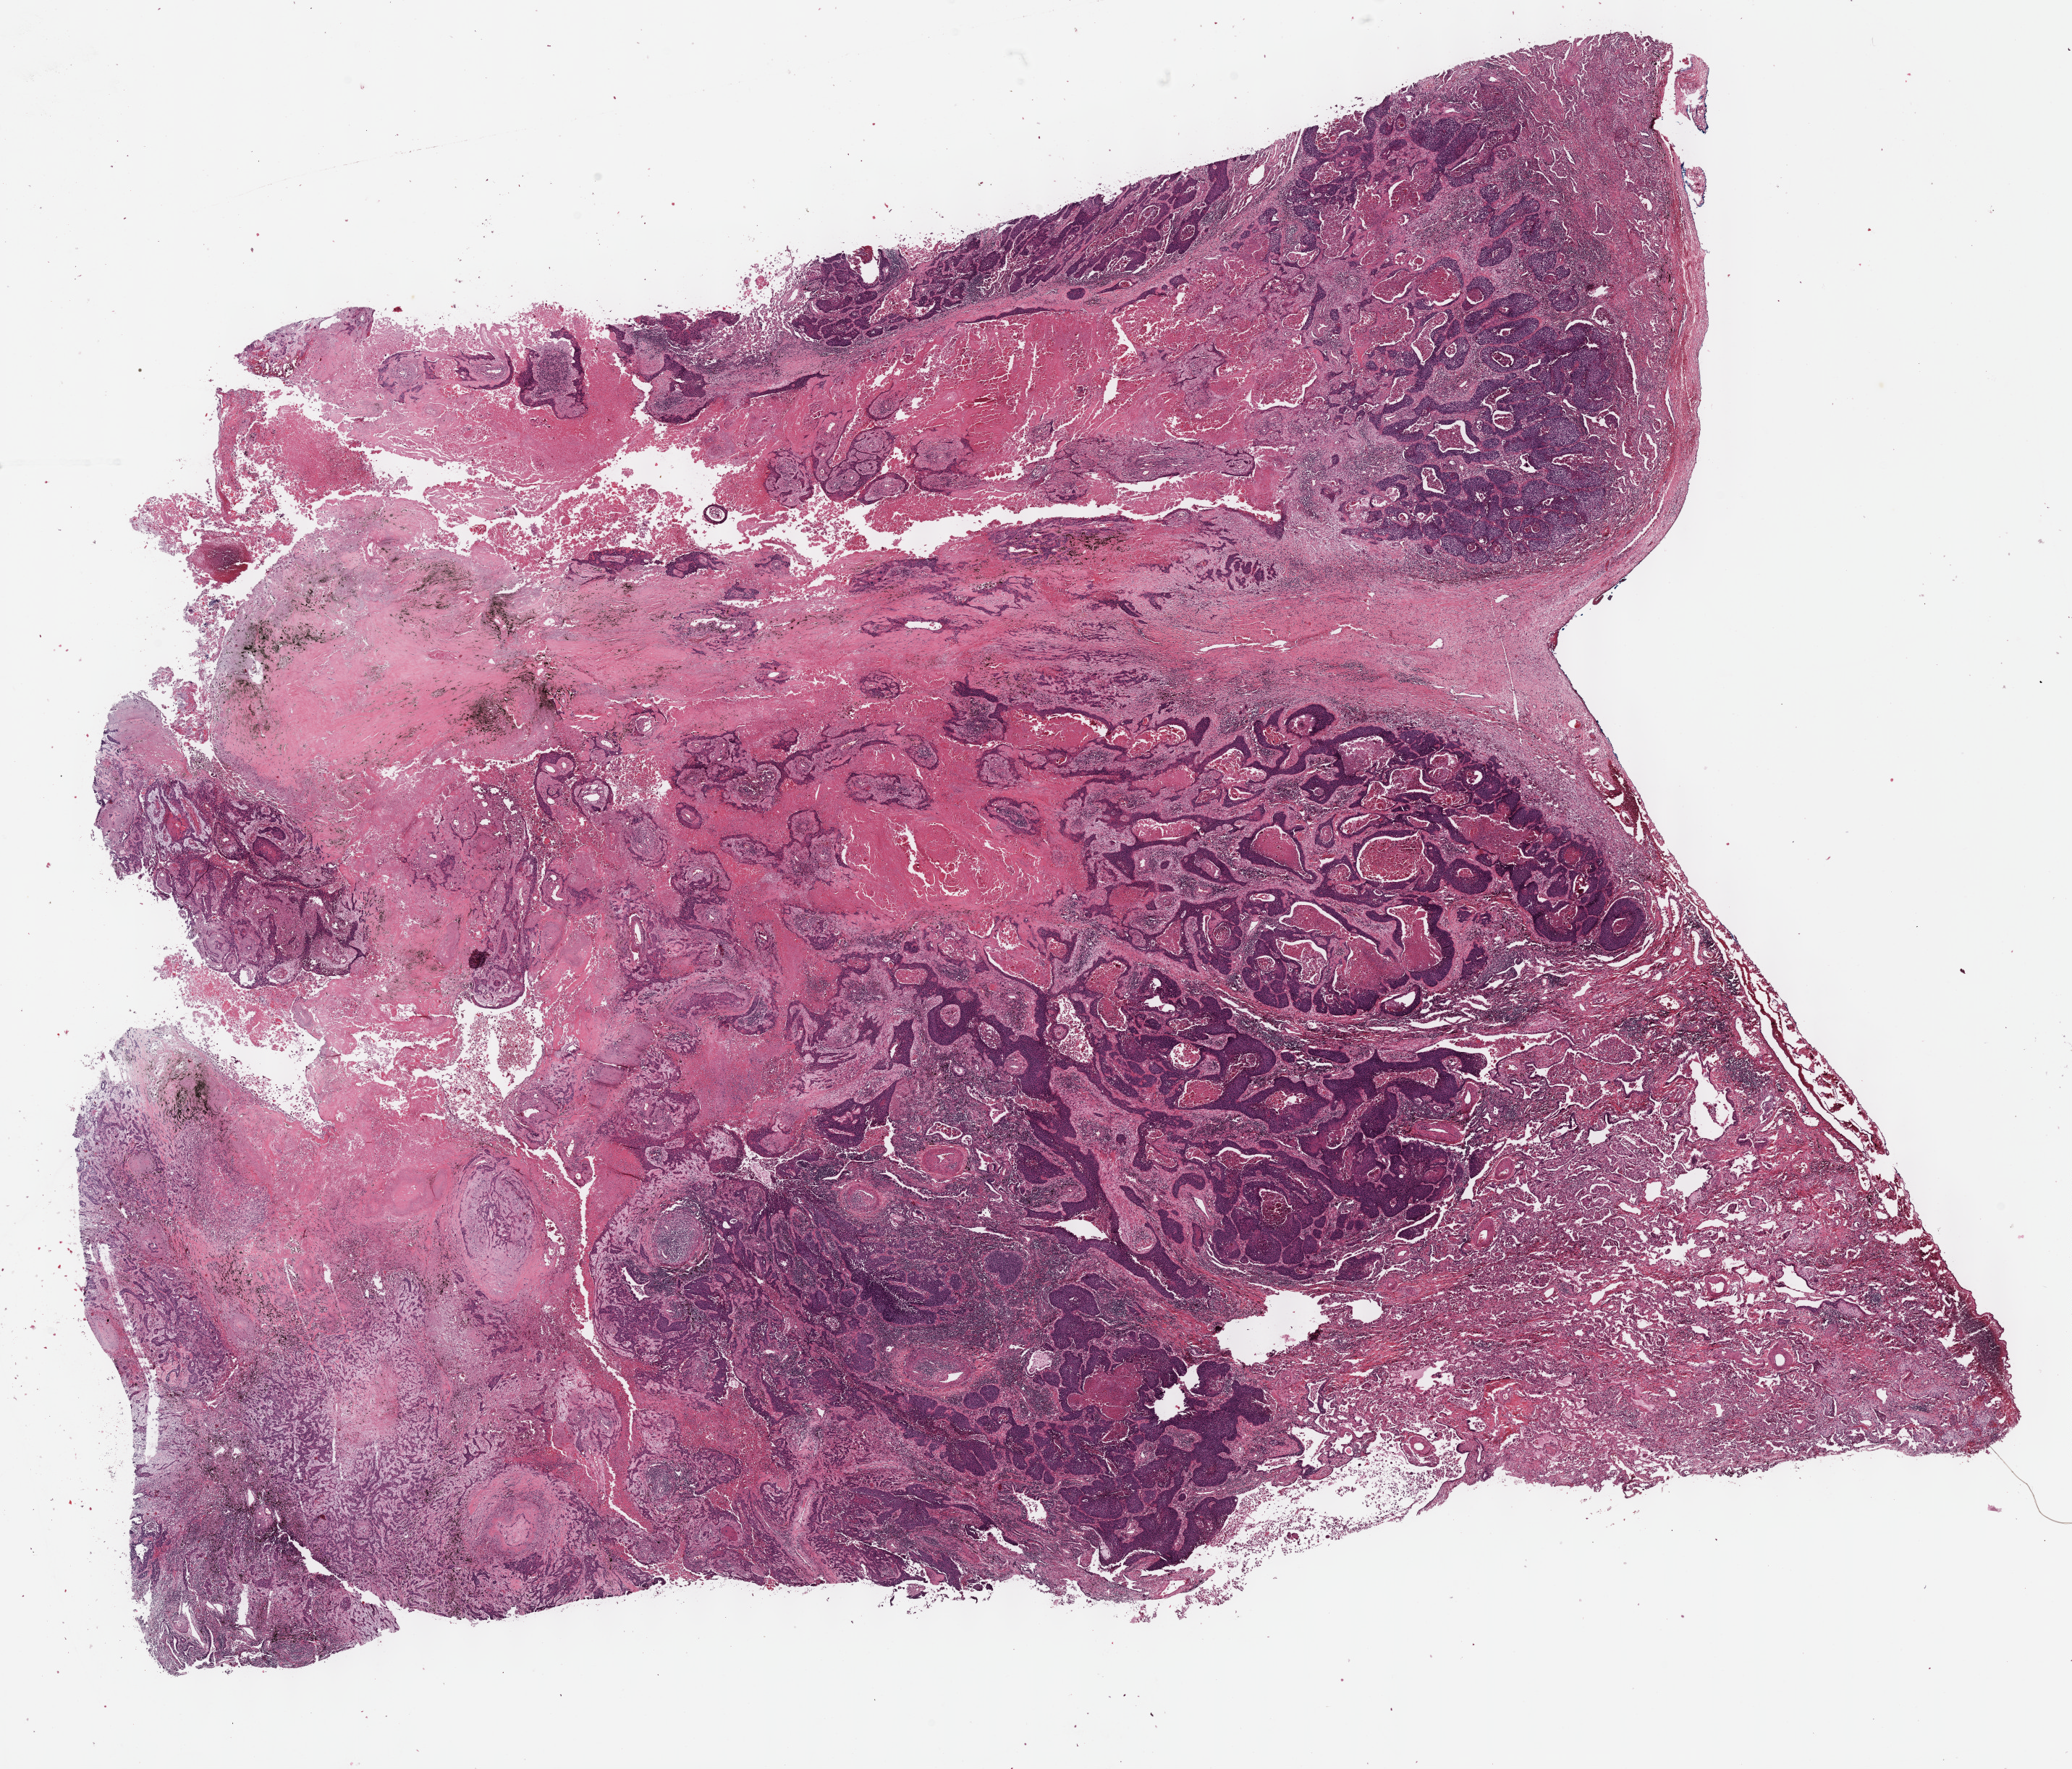
Digitized H&E tissue section (whole slide) — a low-resolution overview of the entire scanned area, about 23.2 x 19.8 mm (slide scanned at 40x); FFPE section; primary tumour sample from the lung. Male patient; age at initial diagnosis 63 years.
- laterality: right
- pathologic diagnosis: Squamous cell carcinoma, NOS (middle lobe, lung)
- AJCC pathologic stage: I (6th edition)